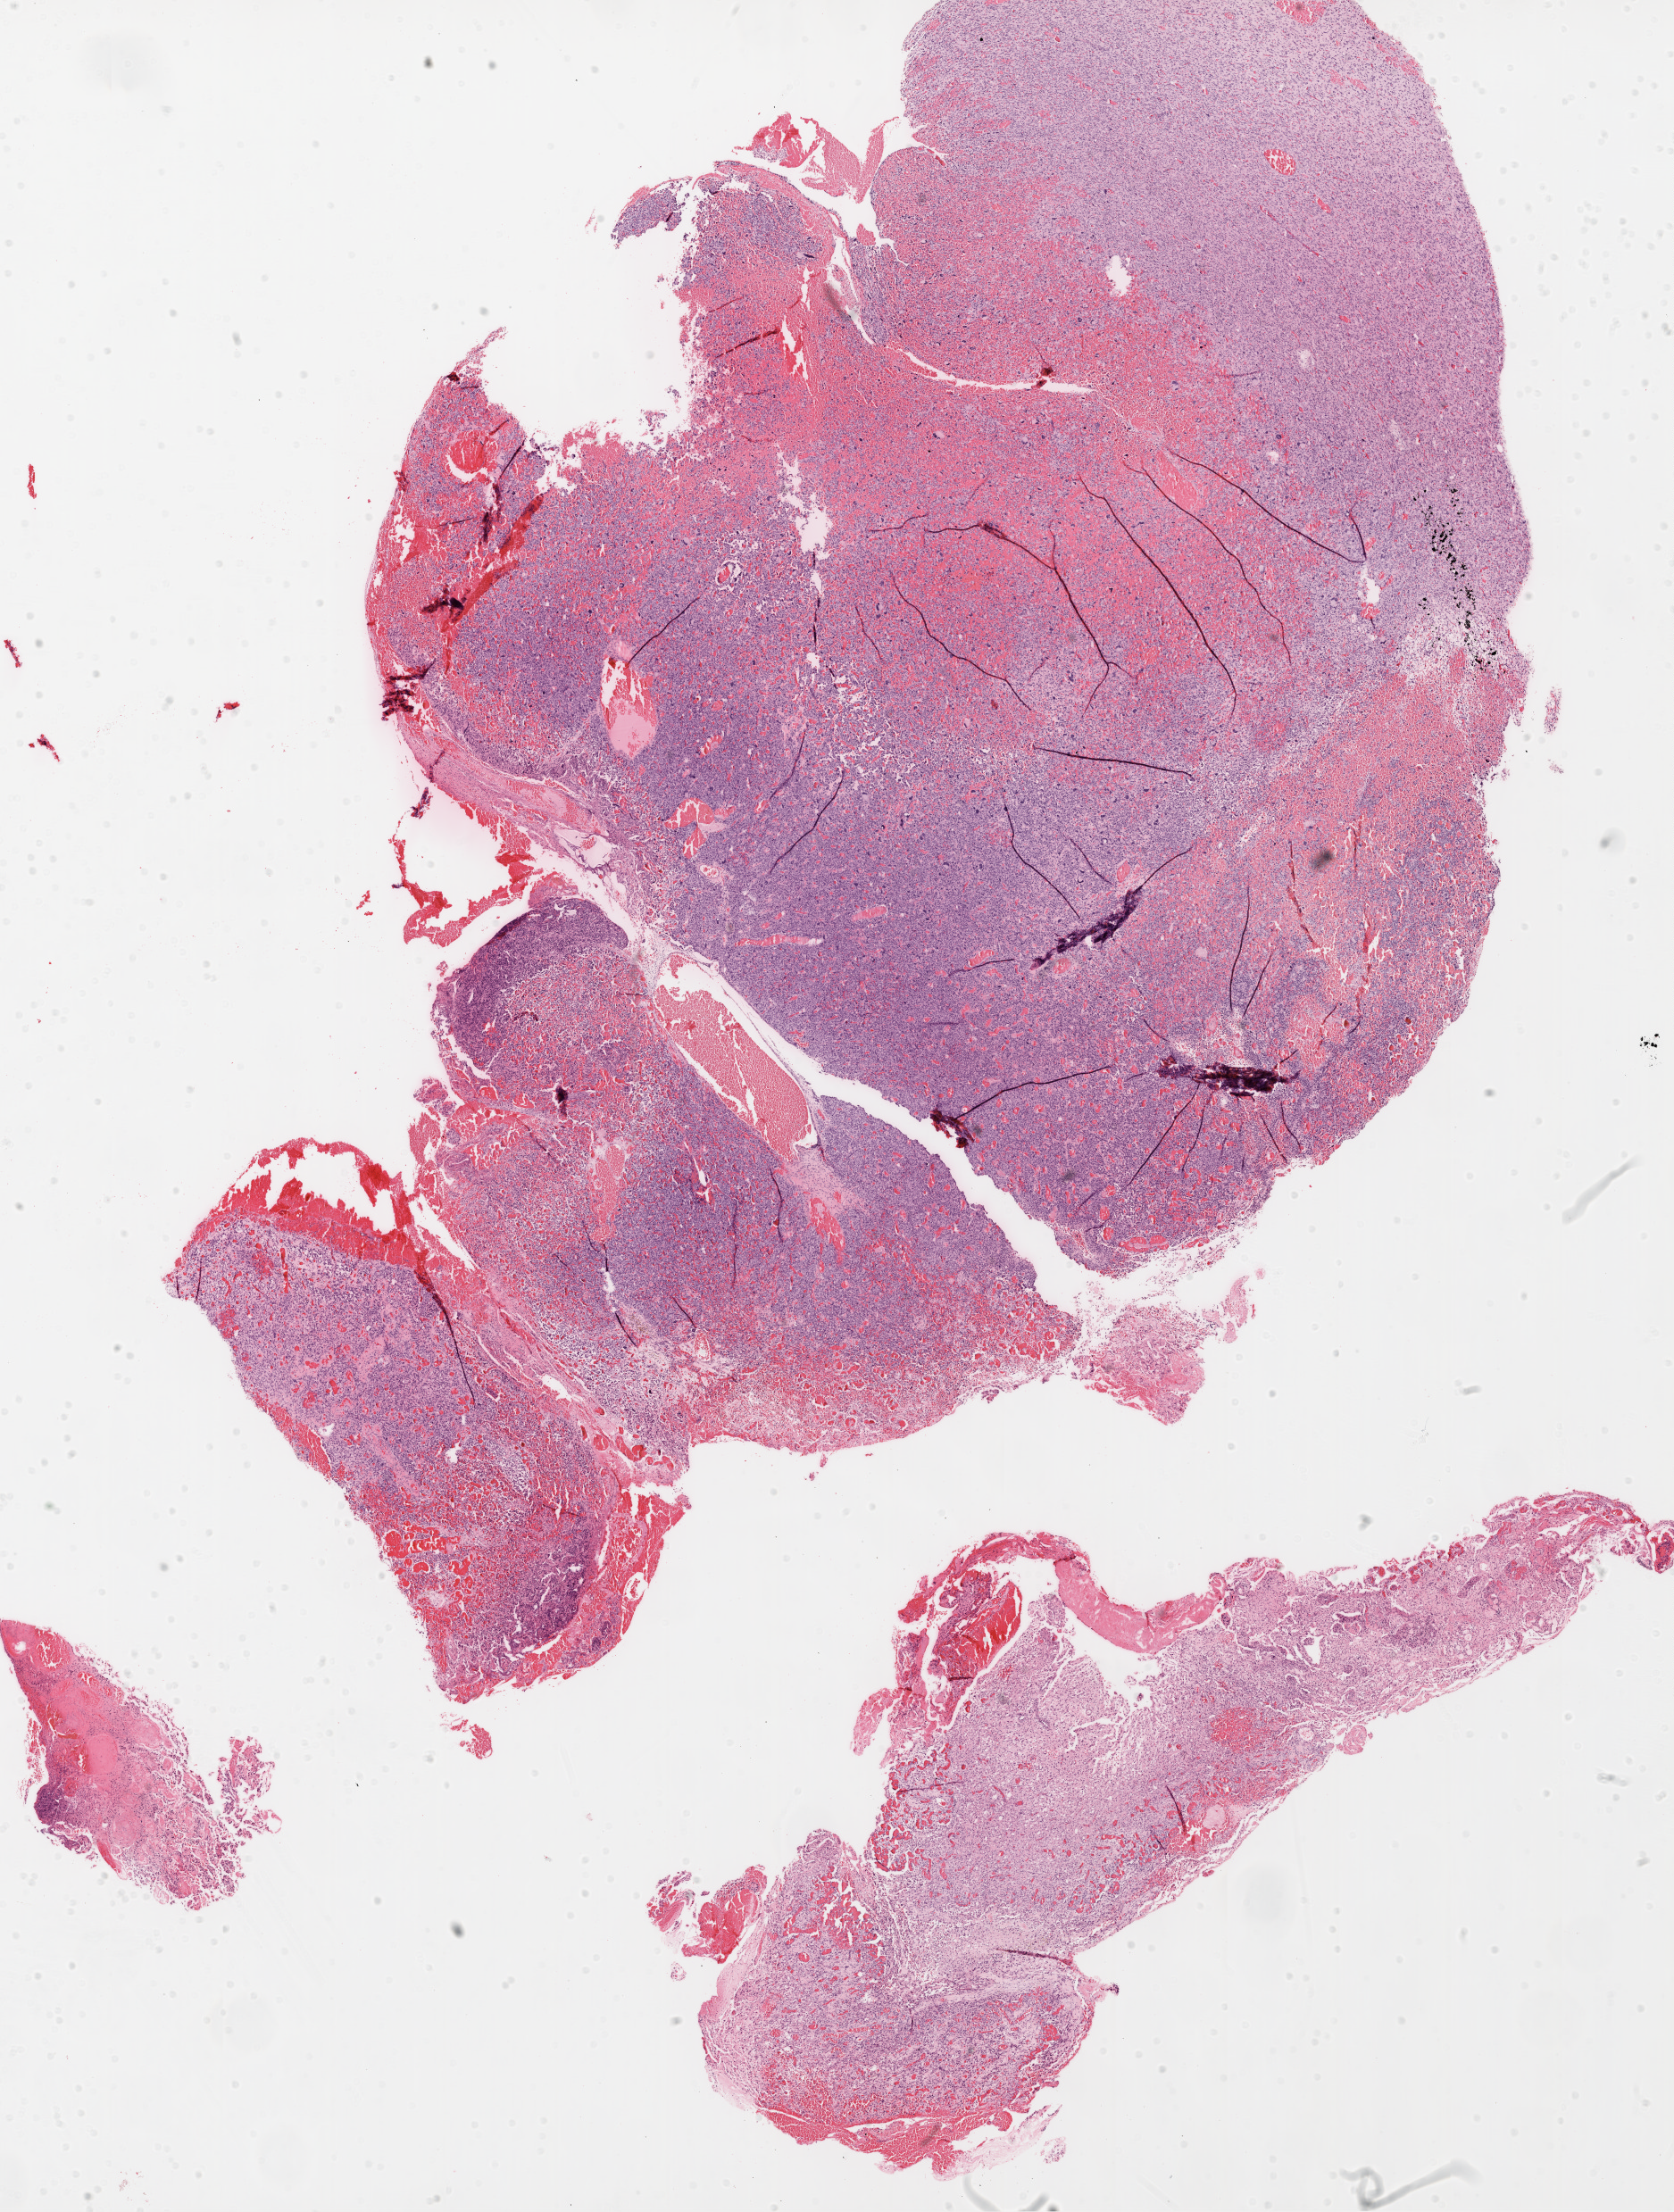
Whole-slide histology image, H&E — low-resolution overview of the scanned area, about 15.0 x 19.9 mm (slide scanned at 20x); formalin-fixed paraffin-embedded (FFPE) diagnostic section; brain, primary tumour sample. Patient: female, age at initial diagnosis 36 years.
Diagnosis: Glioblastoma.